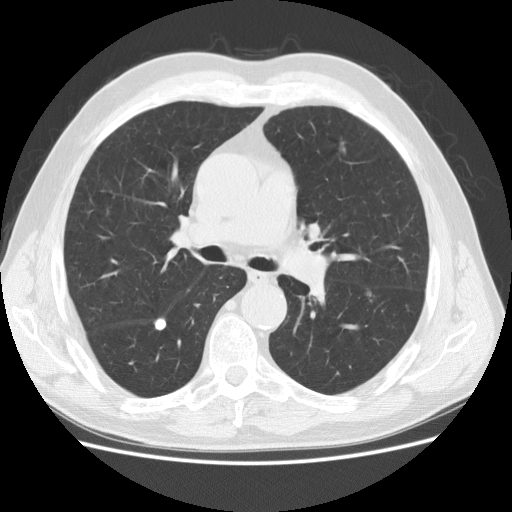
Low-dose screening chest CT, axial slice; first (baseline) screen; lung window (W 1500 / L -600 HU); standard (soft-tissue) reconstruction kernel (STANDARD); slice 66 of 155 in the series. Male participant, aged 73 years at enrolment. Current smoker at enrolment.
Lesion marked by an expert reader, bounding box (x1, y1, x2, y2) in pixels: (351, 279, 389, 307). No non-calcified nodule or mass ≥4 mm was recorded by the screening reader at this exam. Official screen result: negative screen, significant abnormalities not suspicious for lung cancer. Participant outcome: lung cancer diagnosed 536 days after this screen — adenocarcinoma, NOS, left lower lobe, poorly differentiated (G3), stage IIA (AJCC 6th edition), 12 mm at pathology.